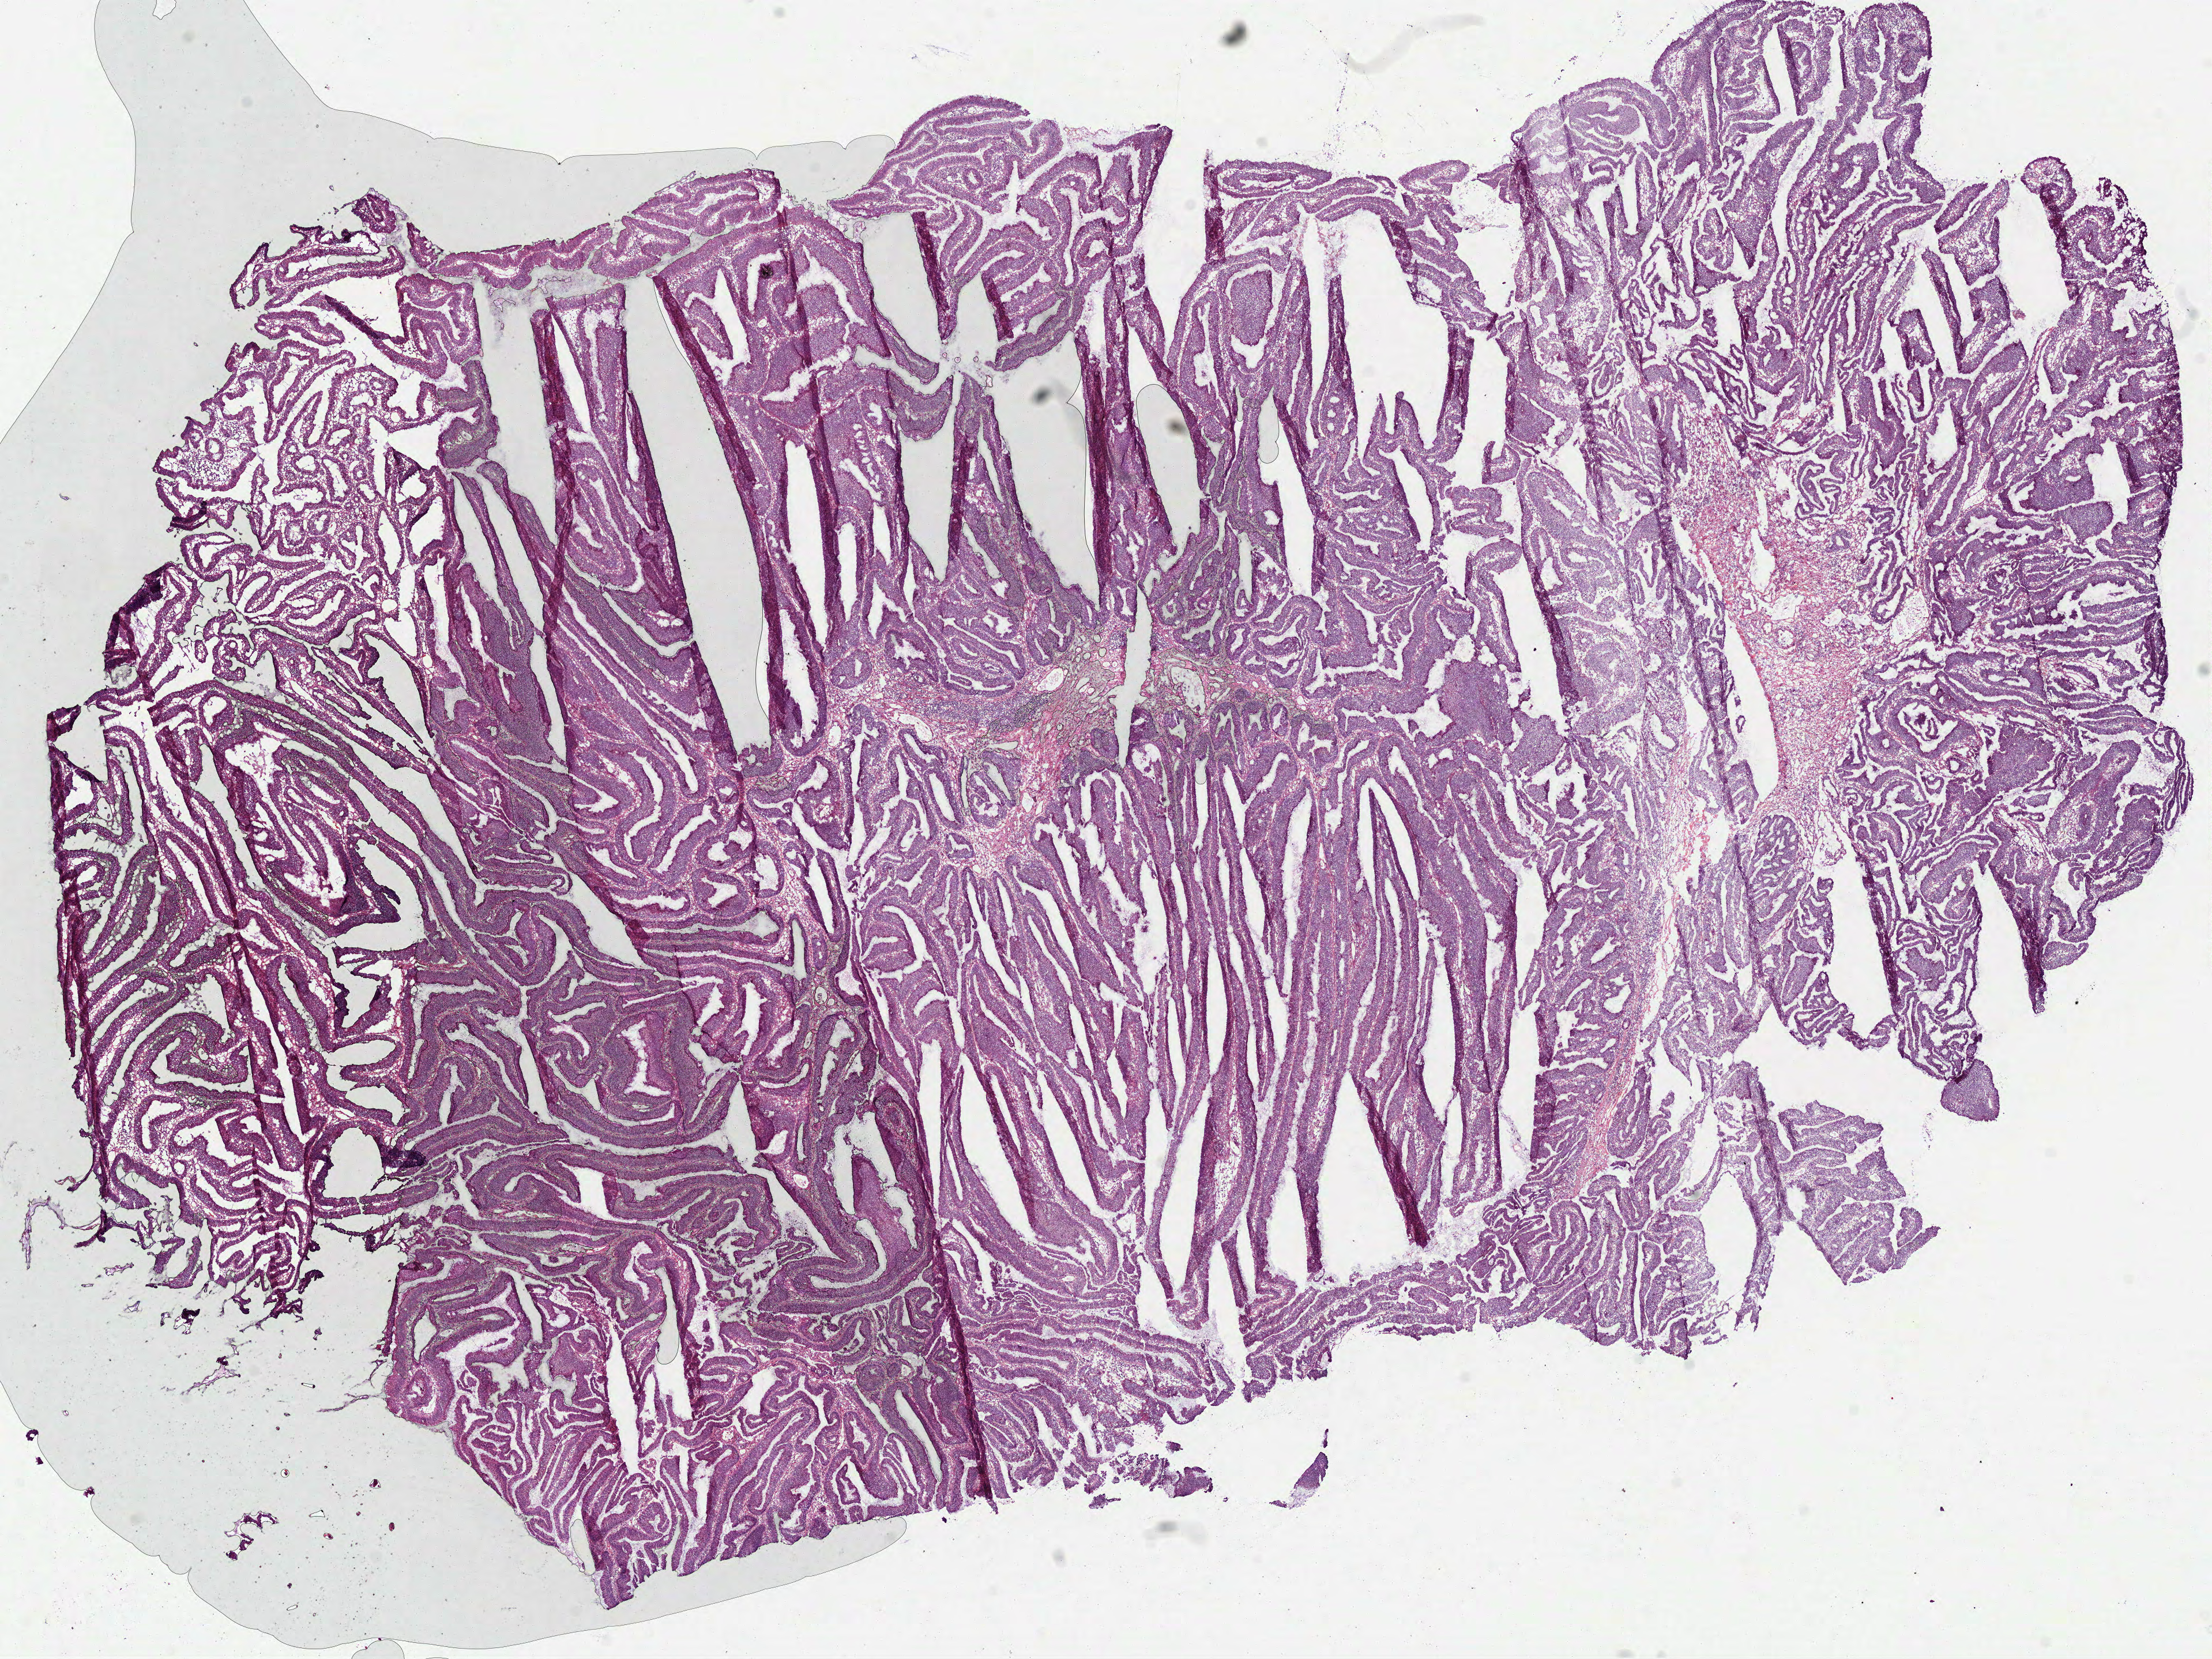
H&E-stained whole-slide image, a low-resolution overview of the entire scanned area, about 15.5 x 11.6 mm. Frozen section from the bottom of the tissue portion. Primary tumour sample from the colon. Patient: male, age at initial diagnosis 72 years. Slide review estimates, as recorded: tumour cells 90%, tumour nuclei 80%, normal cells 0%, stromal cells 10%, necrosis 0%.
- diagnosis: Adenocarcinoma, NOS (cecum)
- AJCC pathologic stage: I (5th edition)